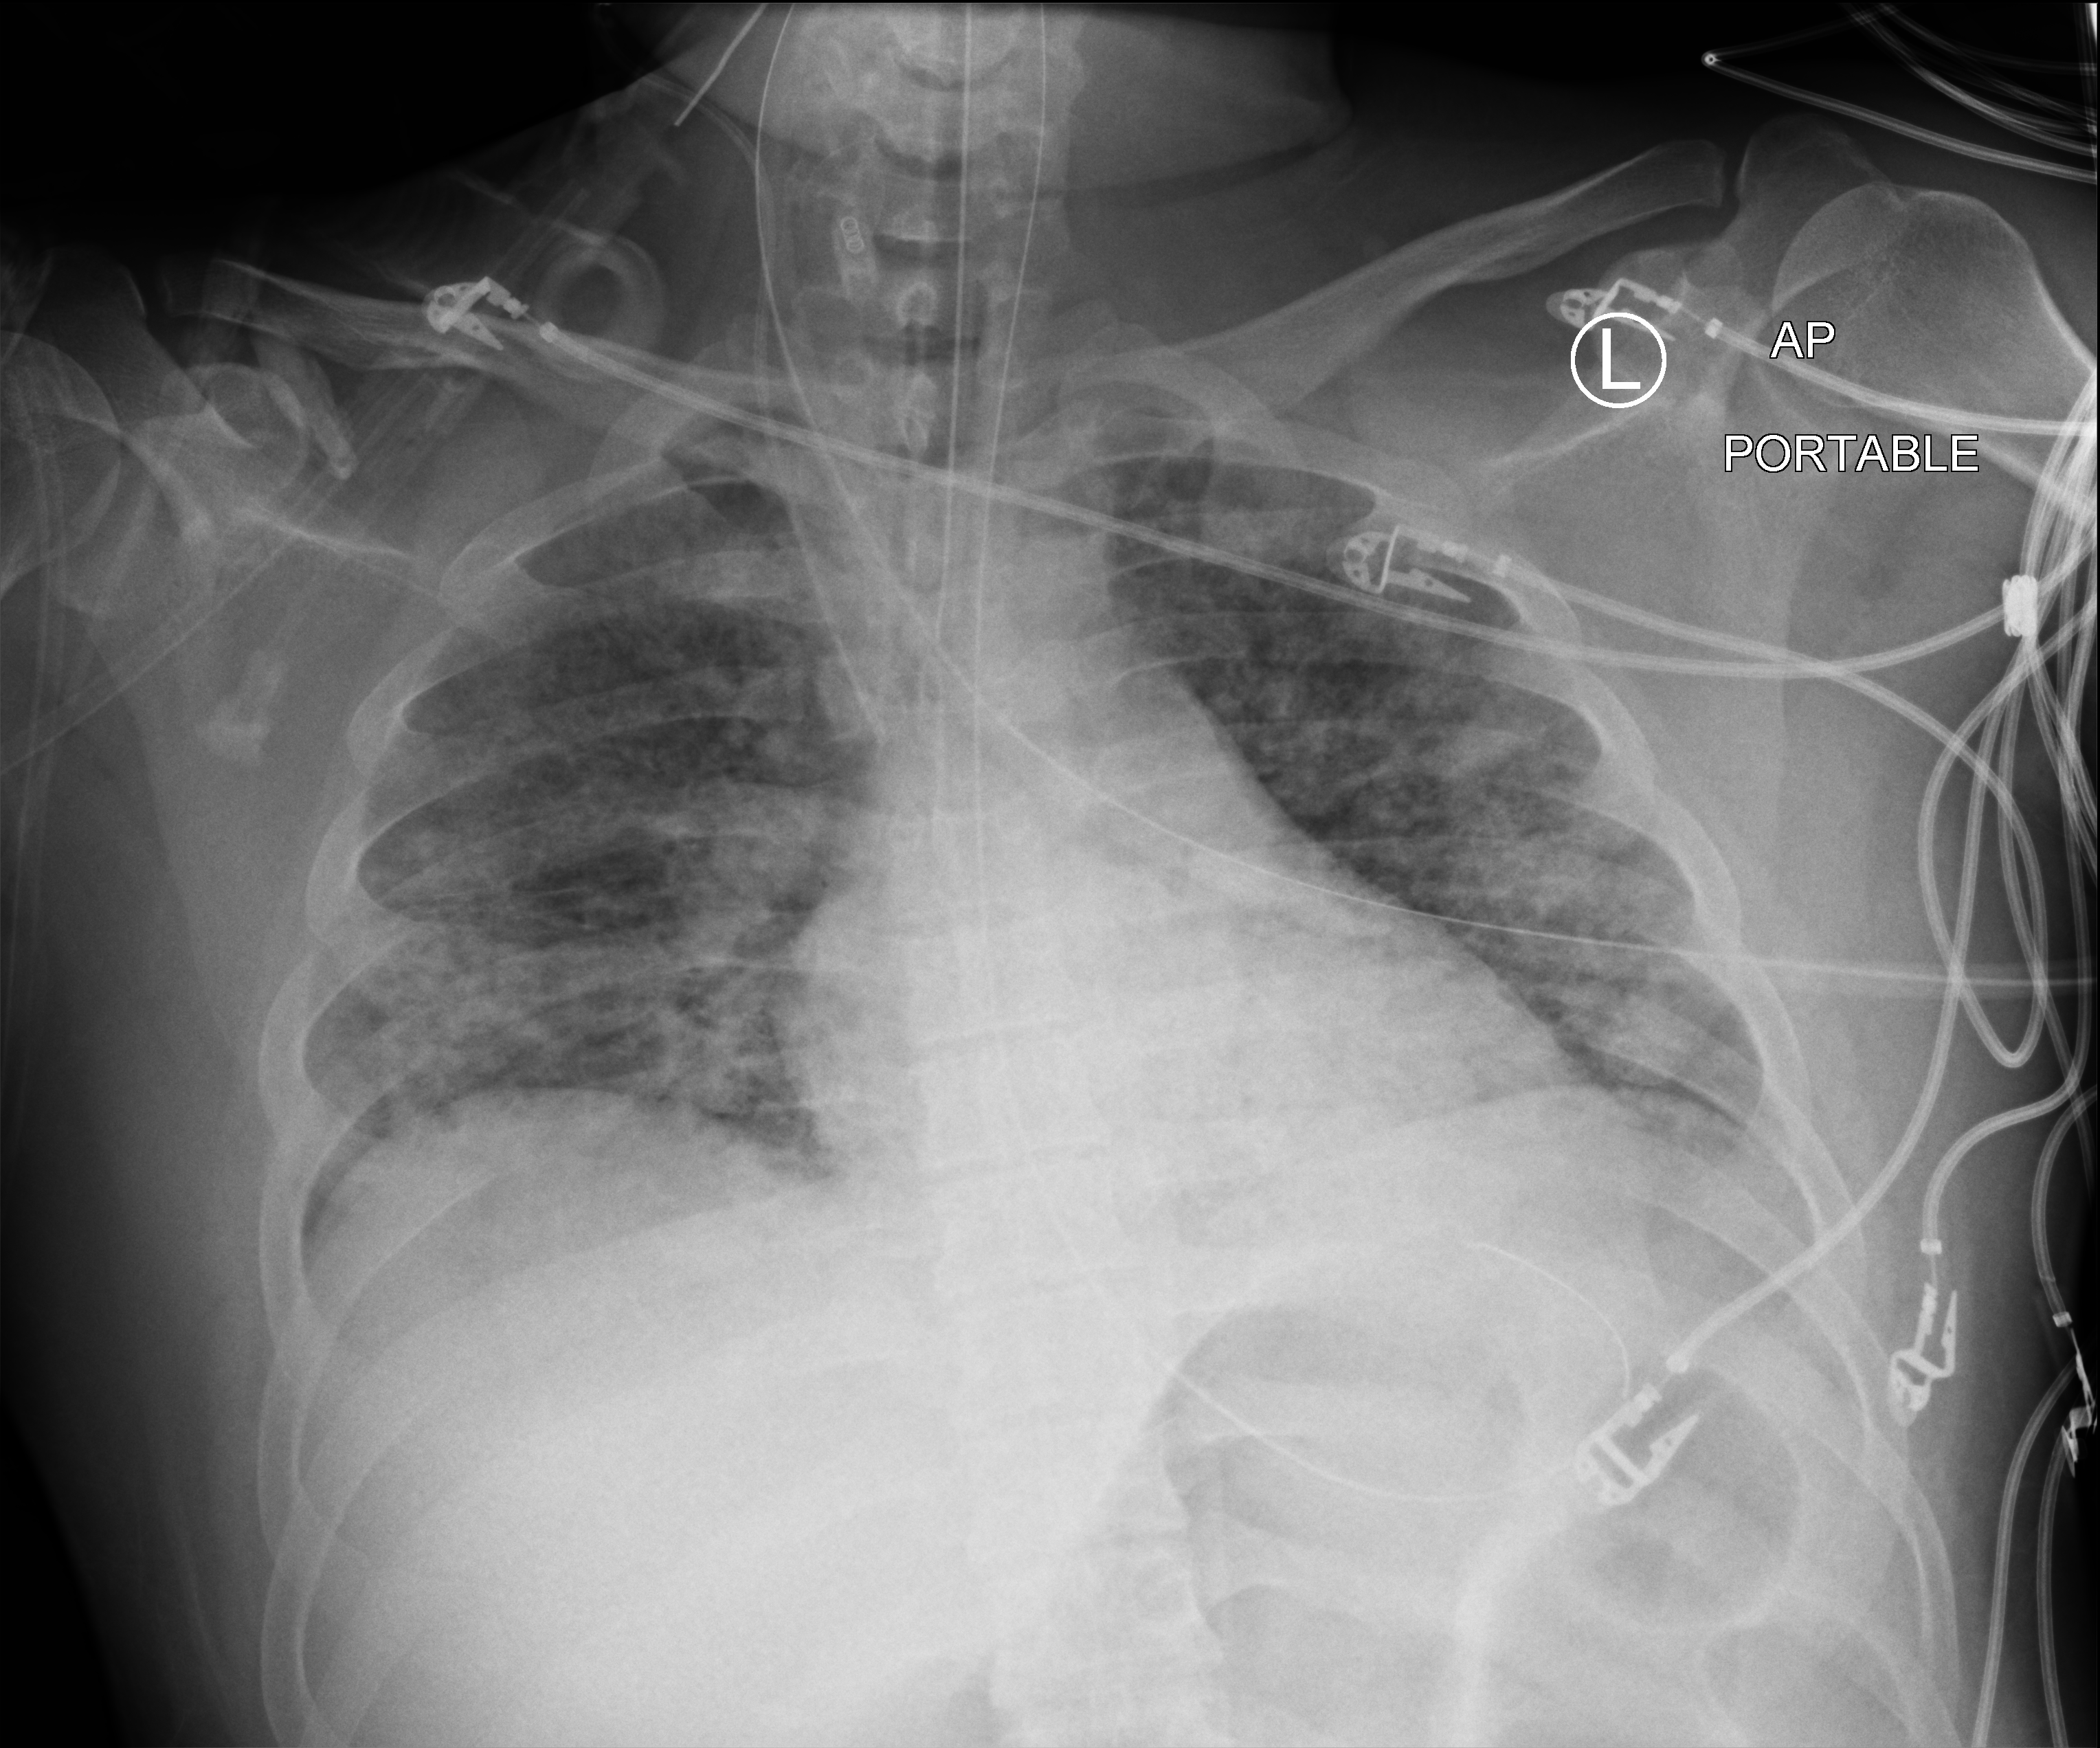
Chest X-ray (portable); anteroposterior (AP) projection. Patient hospitalised with COVID-19; male, aged 18–59 years.
Admission-level facts for this patient (not findings on this image; timing relative to this image not recorded): COPD (admission record): no; mechanically ventilated during this hospital stay: yes; admitted to intensive care during this hospital stay: yes.